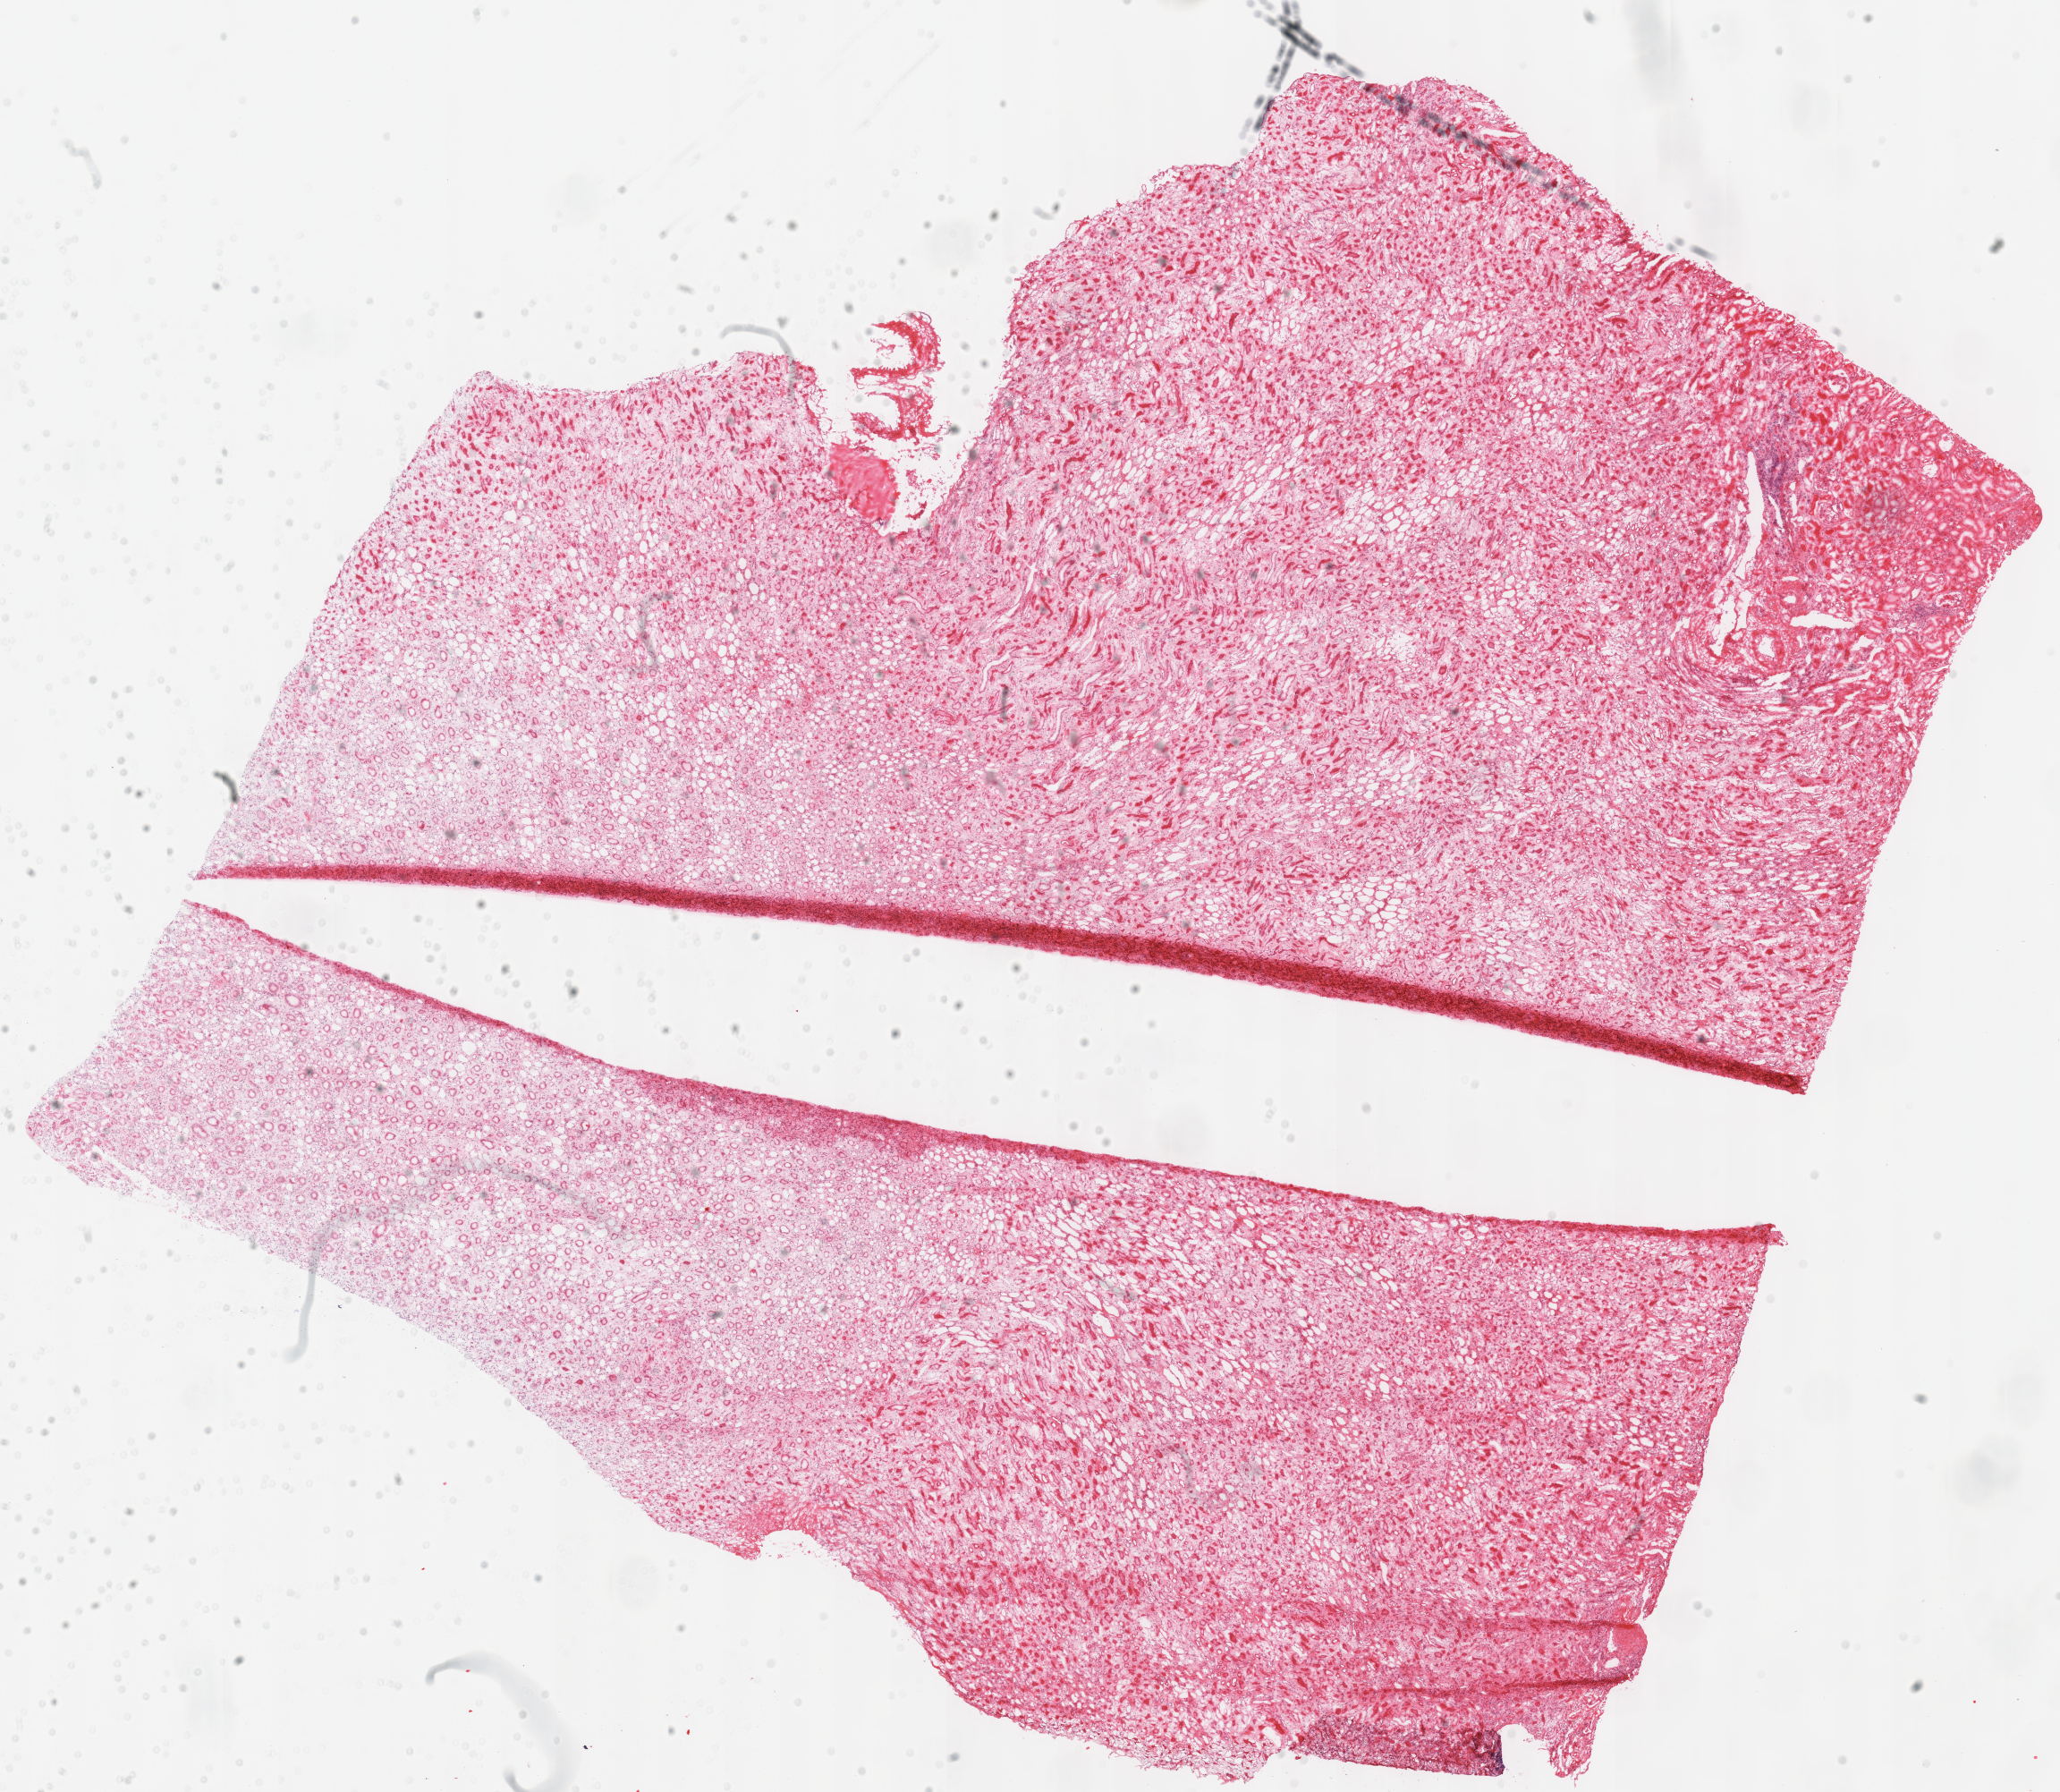
H&E whole-slide image, a low-resolution overview of the entire scanned area, about 18.1 x 15.8 mm. Frozen section. Kidney, solid tissue normal (non-tumour tissue) sample. Male patient; age at initial diagnosis 50 years. Inflammatory infiltration, as recorded: lymphocyte infiltration 5%, monocyte infiltration 0%, neutrophil infiltration 0%.
This section: solid tissue normal (non-tumour) sample from the same patient. Patient diagnosis: Renal cell carcinoma, chromophobe type.